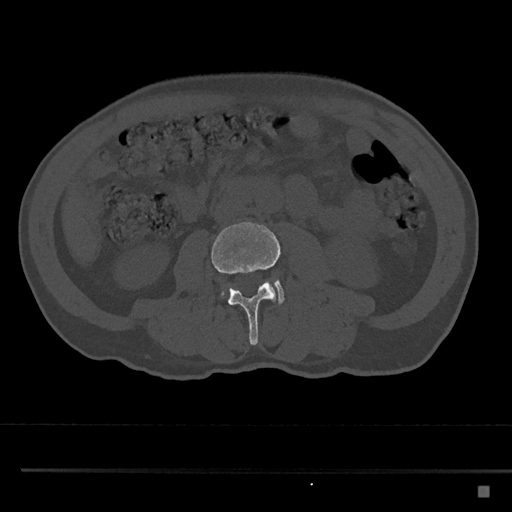
CT including the spine, one axial slice. Position 684 of 797 along the scan axis. Reconstruction kernel Br40s/3. 120 kVp. Bone window (W 1800 / L 400 HU). 512 × 512 image matrix. Patient: male, 59 years. Case-level facts recorded for this patient, not image findings: primary cancer: prostate.
Outlined on this slice (semi-automatic segmentation, software-assisted and operator-edited):
- L3 vertebra: bounding box [x1, y1, x2, y2] px = [211, 221, 281, 345]
- L4 vertebra: [220, 279, 285, 304]